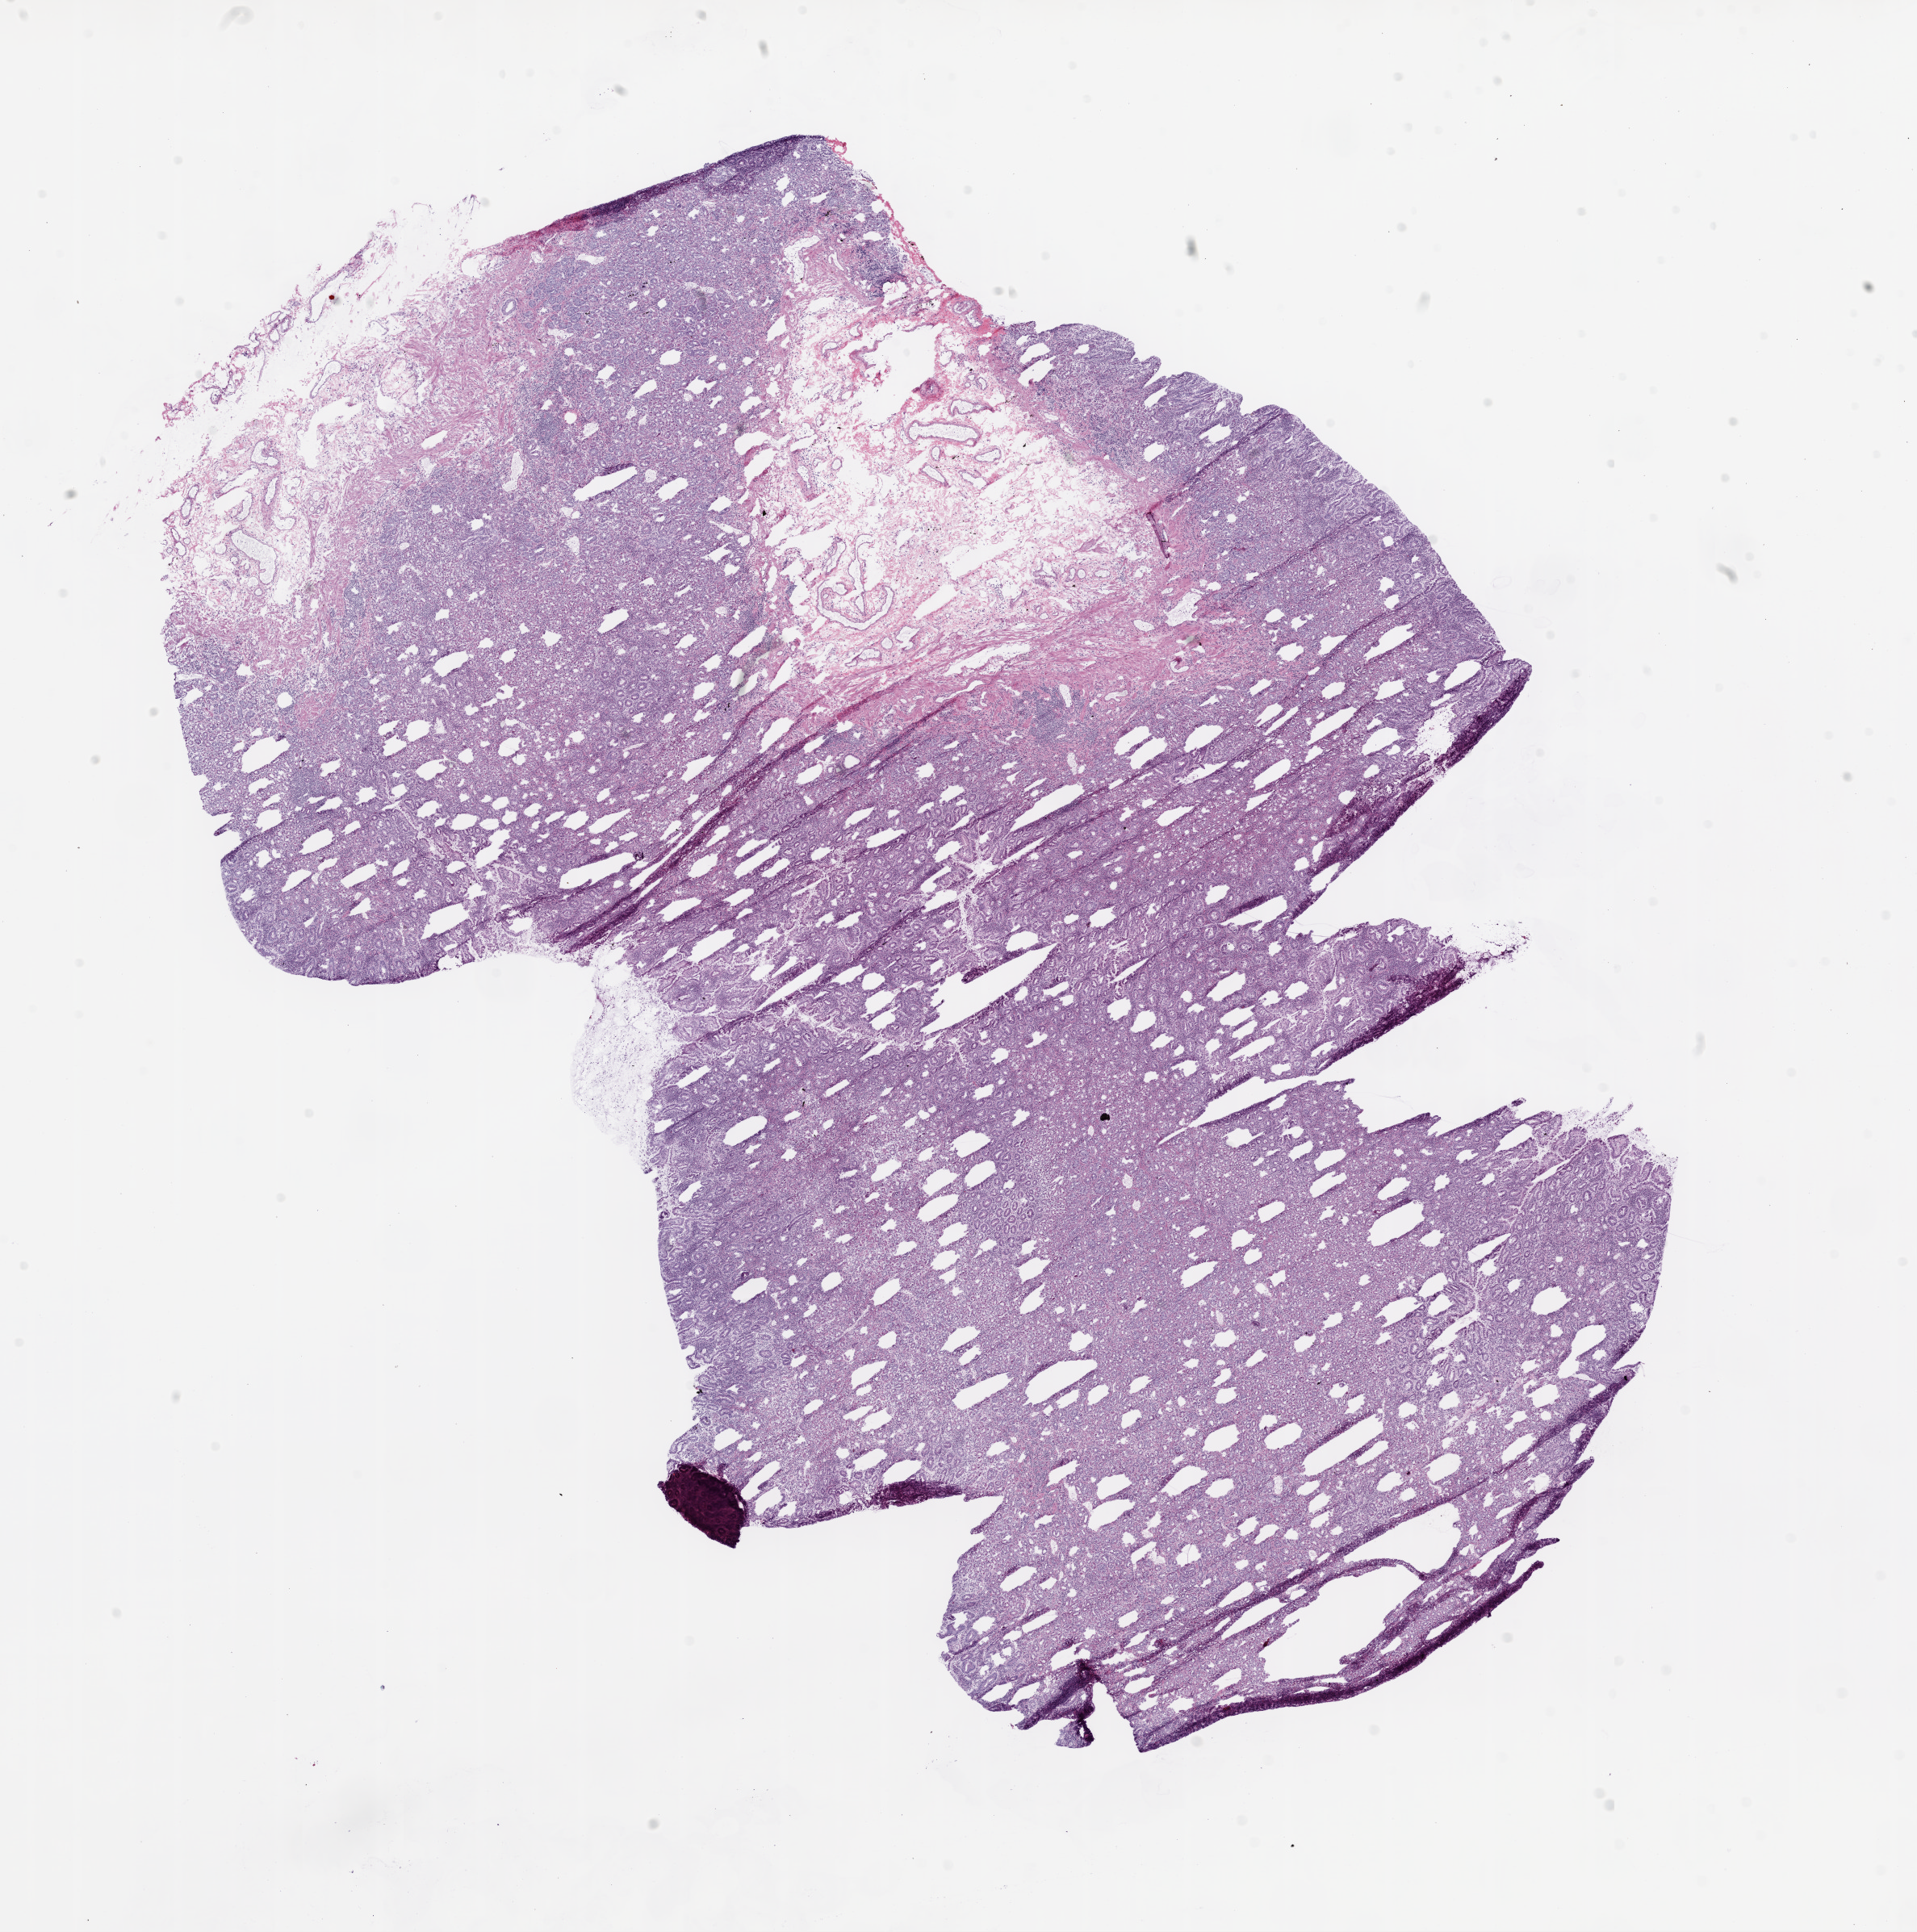
Digitized H&E-stained tissue section (whole slide), whole scanned area (about 19.1 x 19.2 mm) shown as a low-resolution overview. Frozen section from the top of the tissue portion. Sample: solid tissue normal (non-tumour tissue), stomach. Female patient; age at initial diagnosis 66 years.
This section: solid tissue normal sample (biorepository sample class). Patient diagnosis: Adenocarcinoma, NOS.